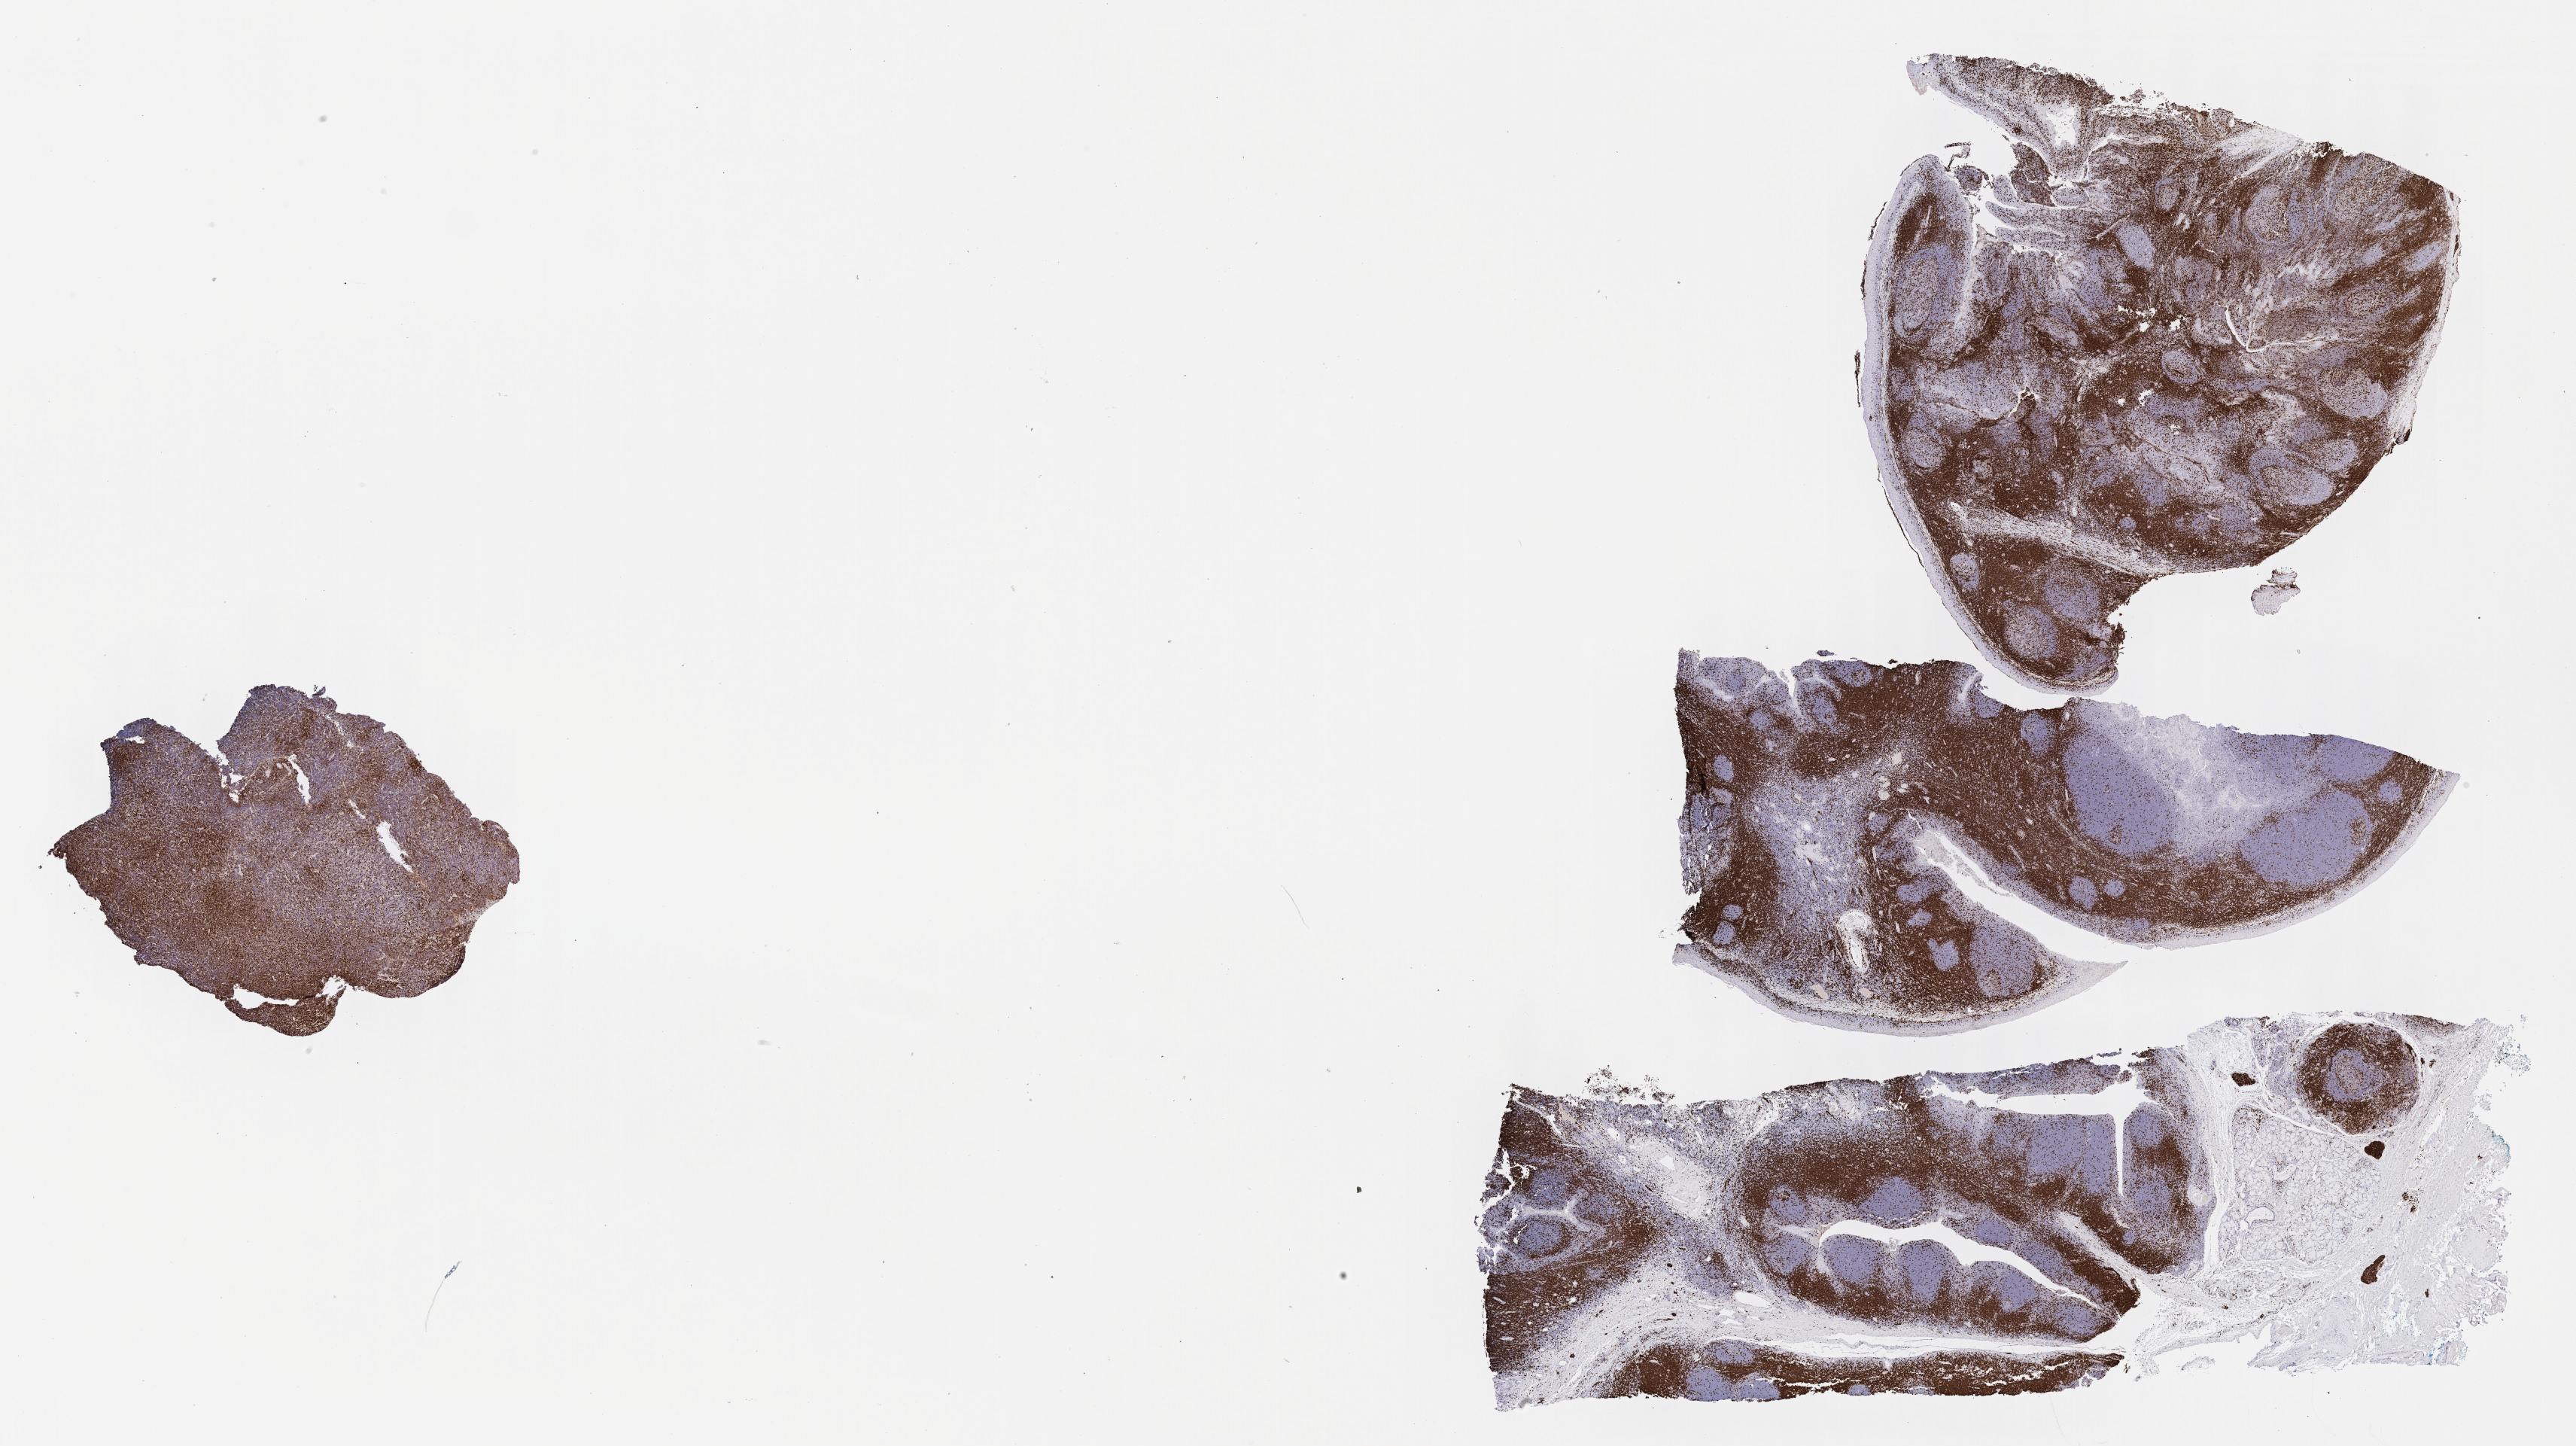
IHC for CD3, whole-slide image, low-resolution overview of the scanned area, about 27.7 x 15.5 mm. Specimen: tumor tissue. Anatomic site: mandible. Male, age 8 years at initial diagnosis.
Diagnosis: Burkitt lymphoma, NOS.